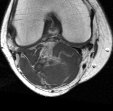
MRI of an extremity soft-tissue mass, one axial slice; position 13 of 45 along the scan axis; MR volume resampled by the dataset authors to the PET/CT grid (not the native acquisition matrix); 3.27 mm slice thickness; 113 × 111 image matrix. Female patient. From the clinical record (not read from this slice): histological type: liposarcoma; site of the primary tumour: right thigh.
Structures marked on this image (expert contour drawn on MRI and transferred to this co-registered scan by the dataset authors):
- gross tumour volume (mass): bounding box (x1, y1, x2, y2) in pixels: (31, 56, 70, 86)